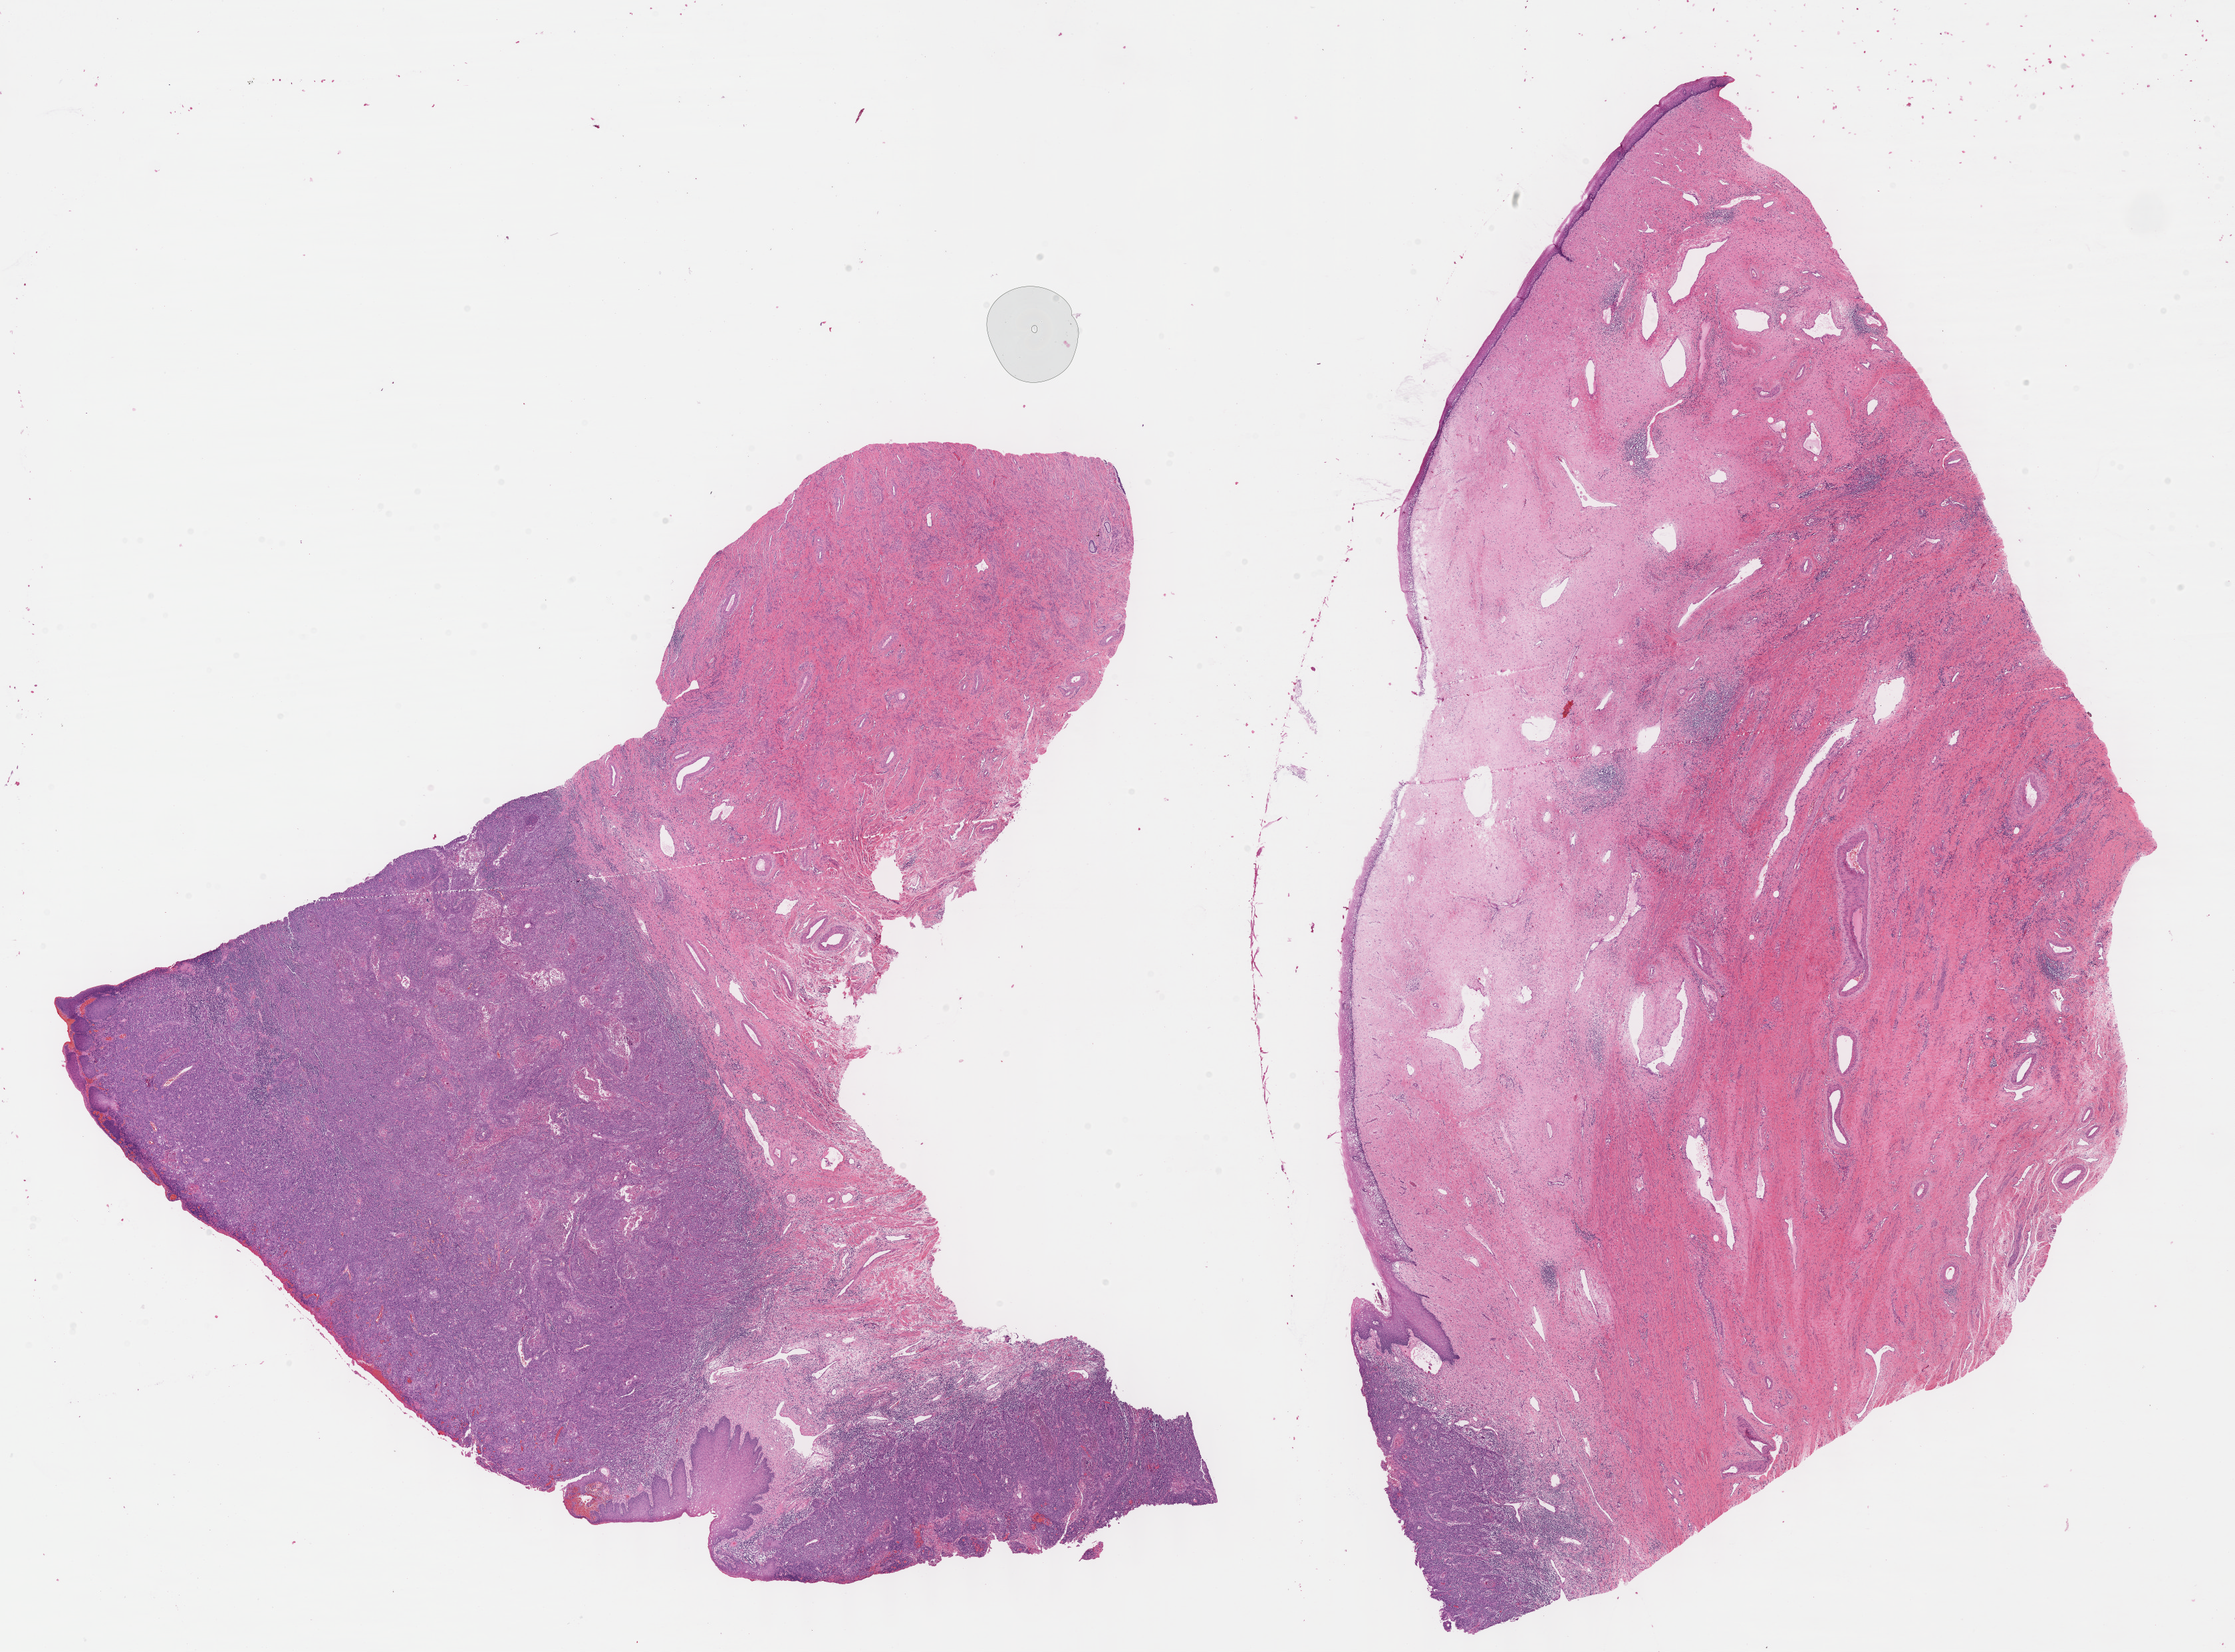
Digitized H&E-stained tissue section (whole slide) — low-resolution overview of the scanned area, about 27.2 x 20.1 mm (from a 40x scan), formalin-fixed paraffin-embedded (FFPE) diagnostic section, sample: primary tumour, cervix. Patient: female, age at initial diagnosis 48 years. Histologic grade: G3 (poorly differentiated).
Lymph nodes positive (case pathology): 0 of 29 examined. FIGO stage: IB1. Histologic diagnosis: Squamous cell carcinoma, keratinizing, NOS (cervix uteri).